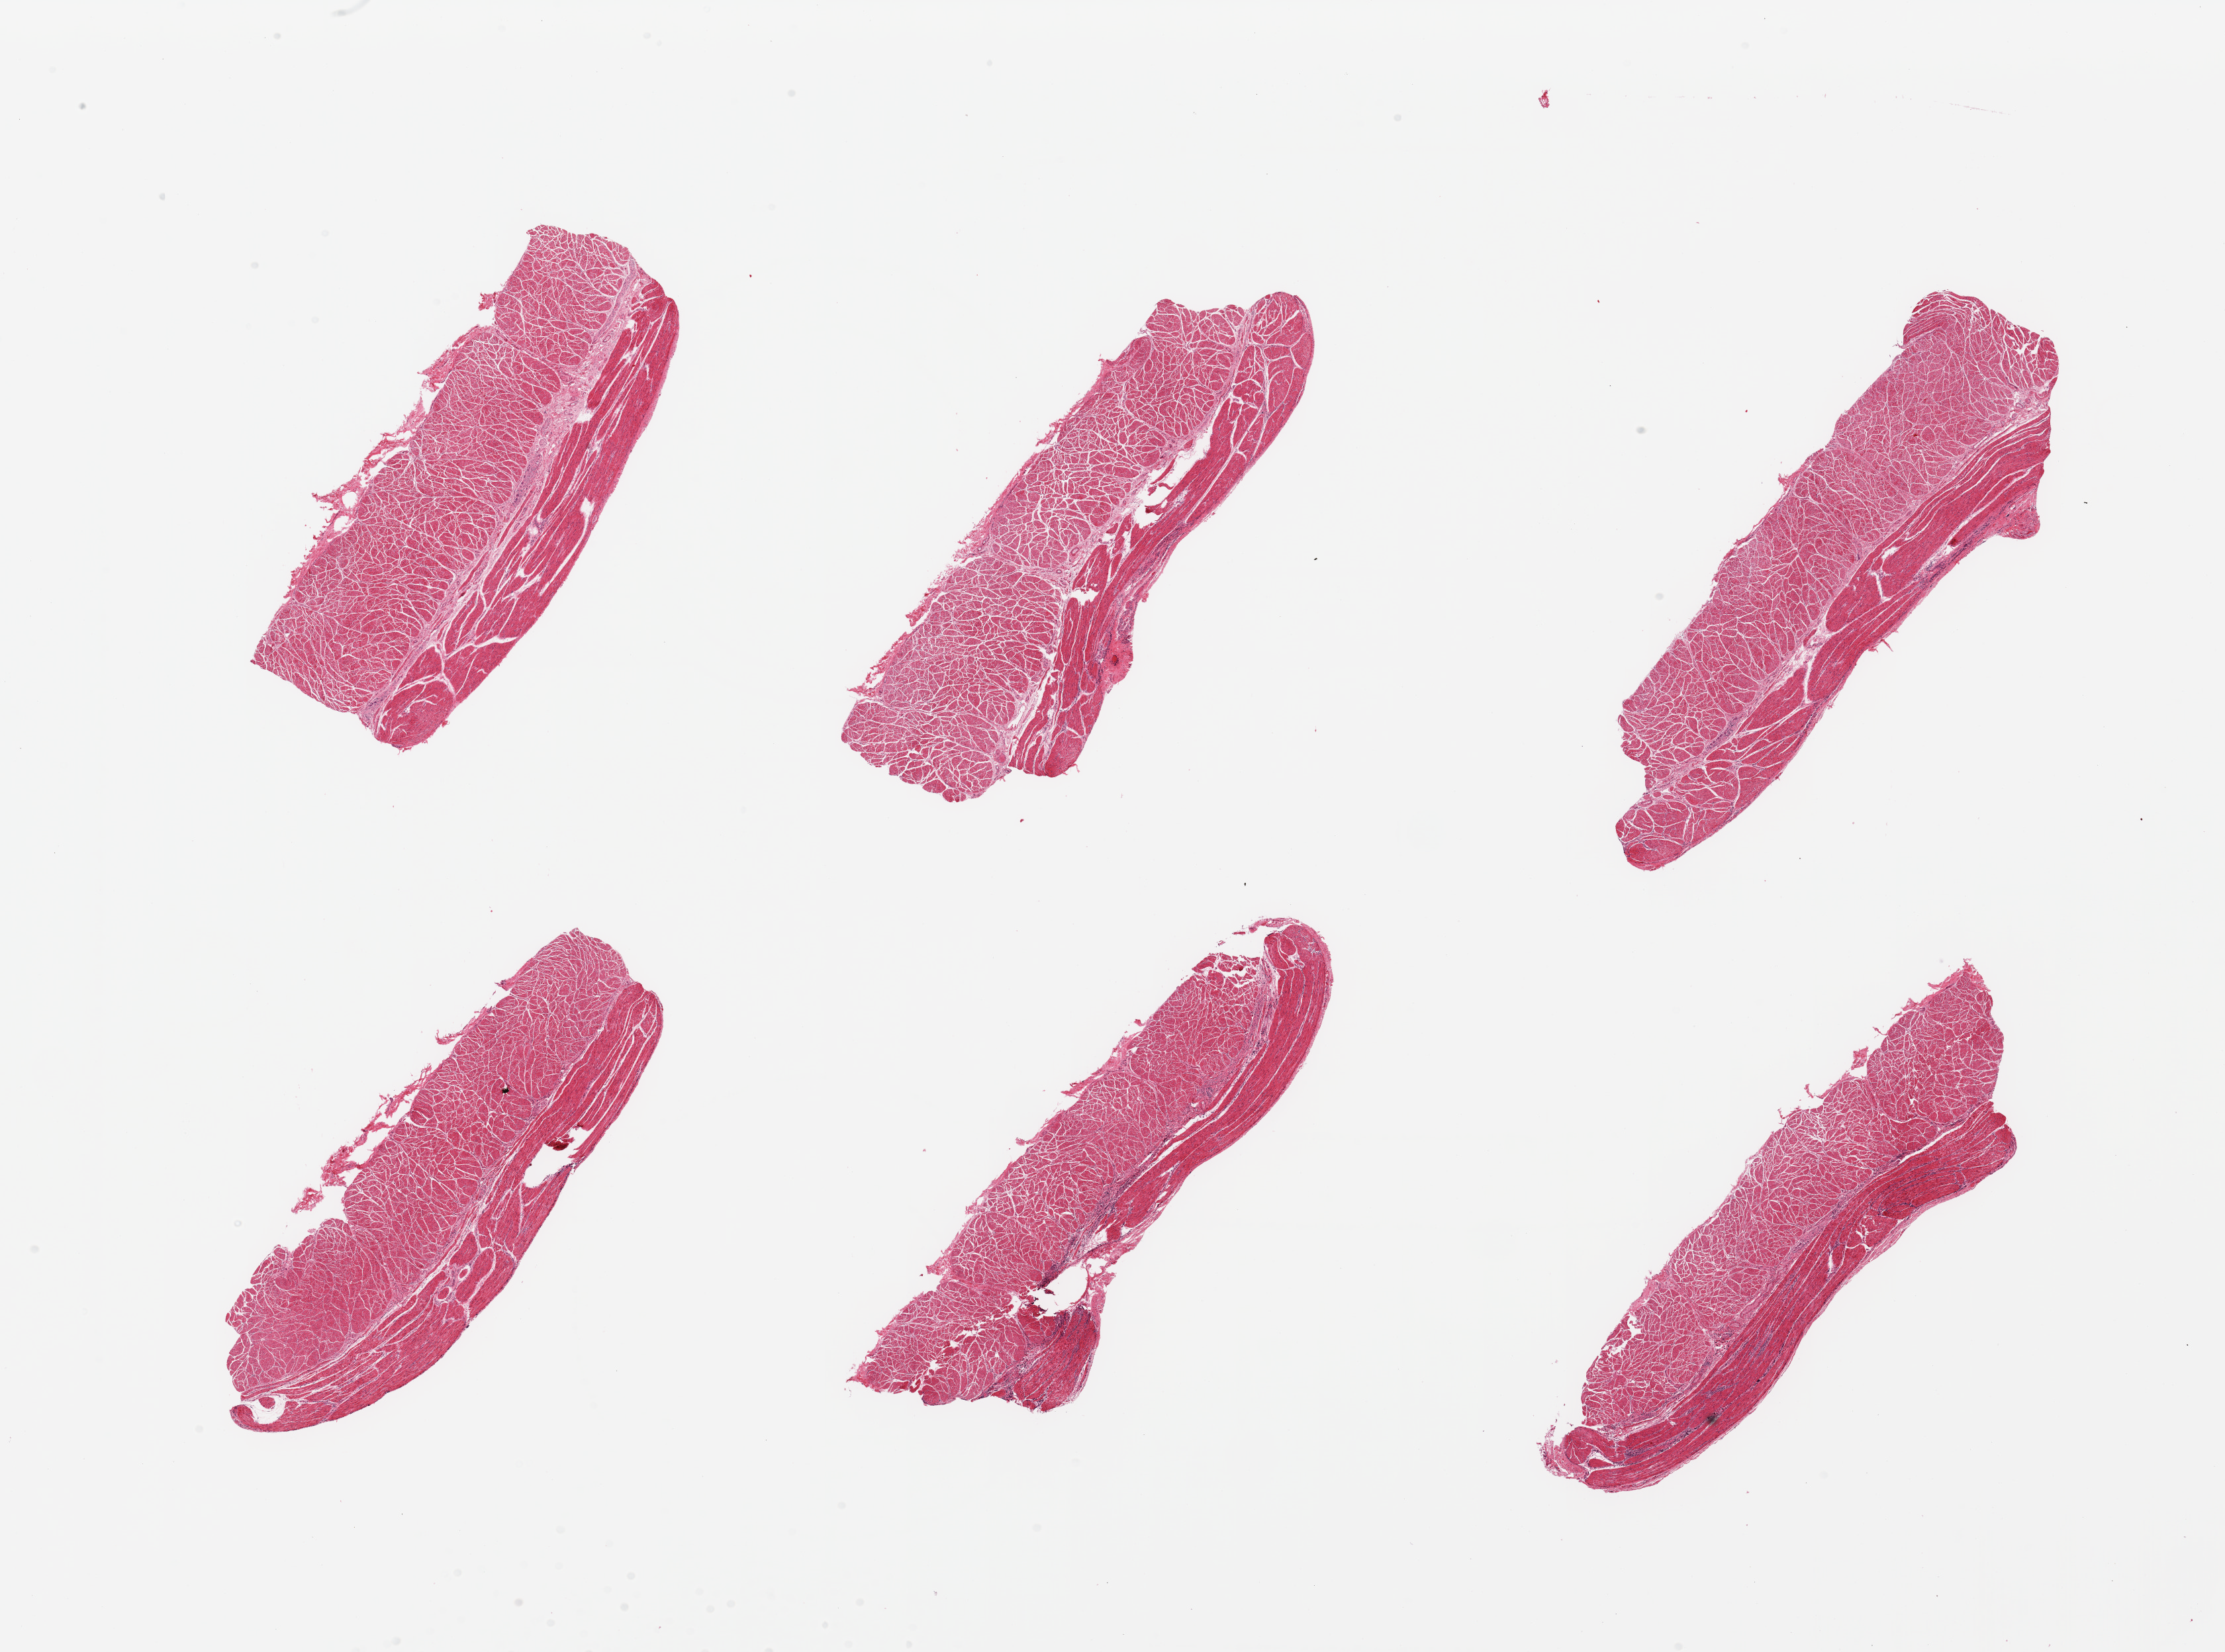
Whole-slide image, haematoxylin and eosin stain — shown as a low-resolution overview of the whole scanned area (about 26.6 x 19.7 mm), PAXgene-fixed paraffin-embedded (PFPE) section, section of esophageal muscle (target tissue), tissue donor sample. Female donor.
Pathologist's review note for this sample: 6 pieces; well dissected muscle.